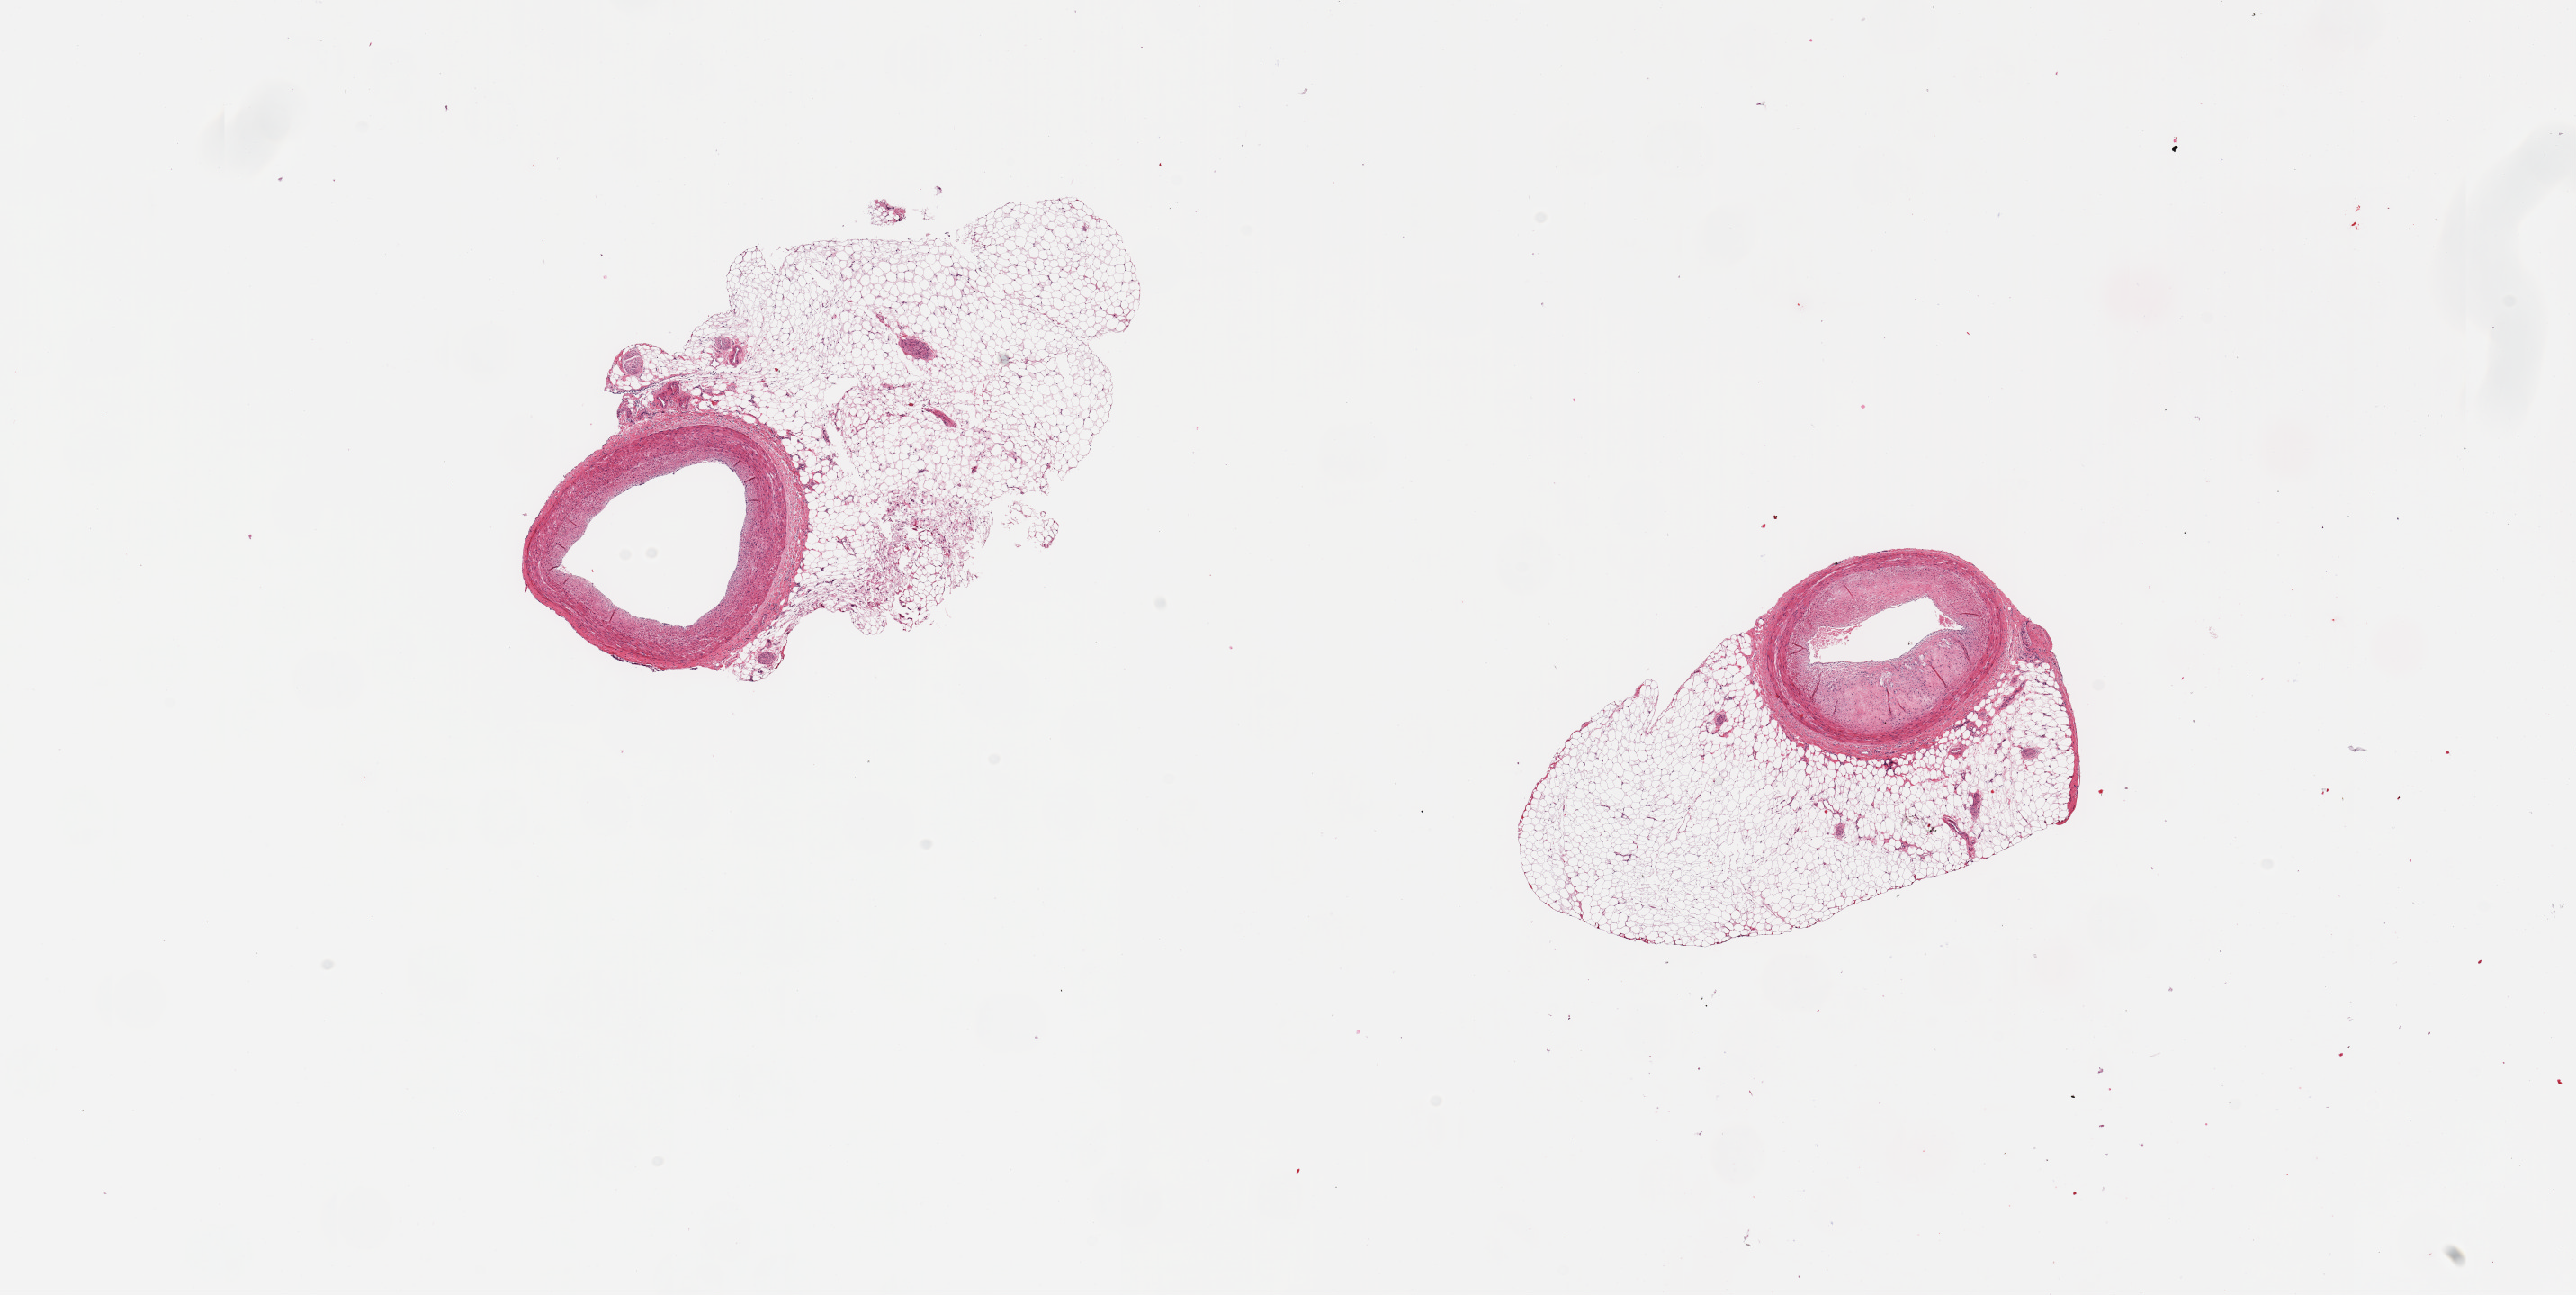
Haematoxylin and eosin whole-slide image, brightfield — low-resolution overview of the scanned area, about 22.6 x 11.4 mm (acquisition: 20x scan); PAXgene-fixed paraffin-embedded (PFPE) section; sampled site (target tissue): coronary artery; donor tissue sample. Donor: male.
- review note (as recorded): 2 pieces; large [50%] intimal plaque in 1 piece, none in other; 60% is external fat